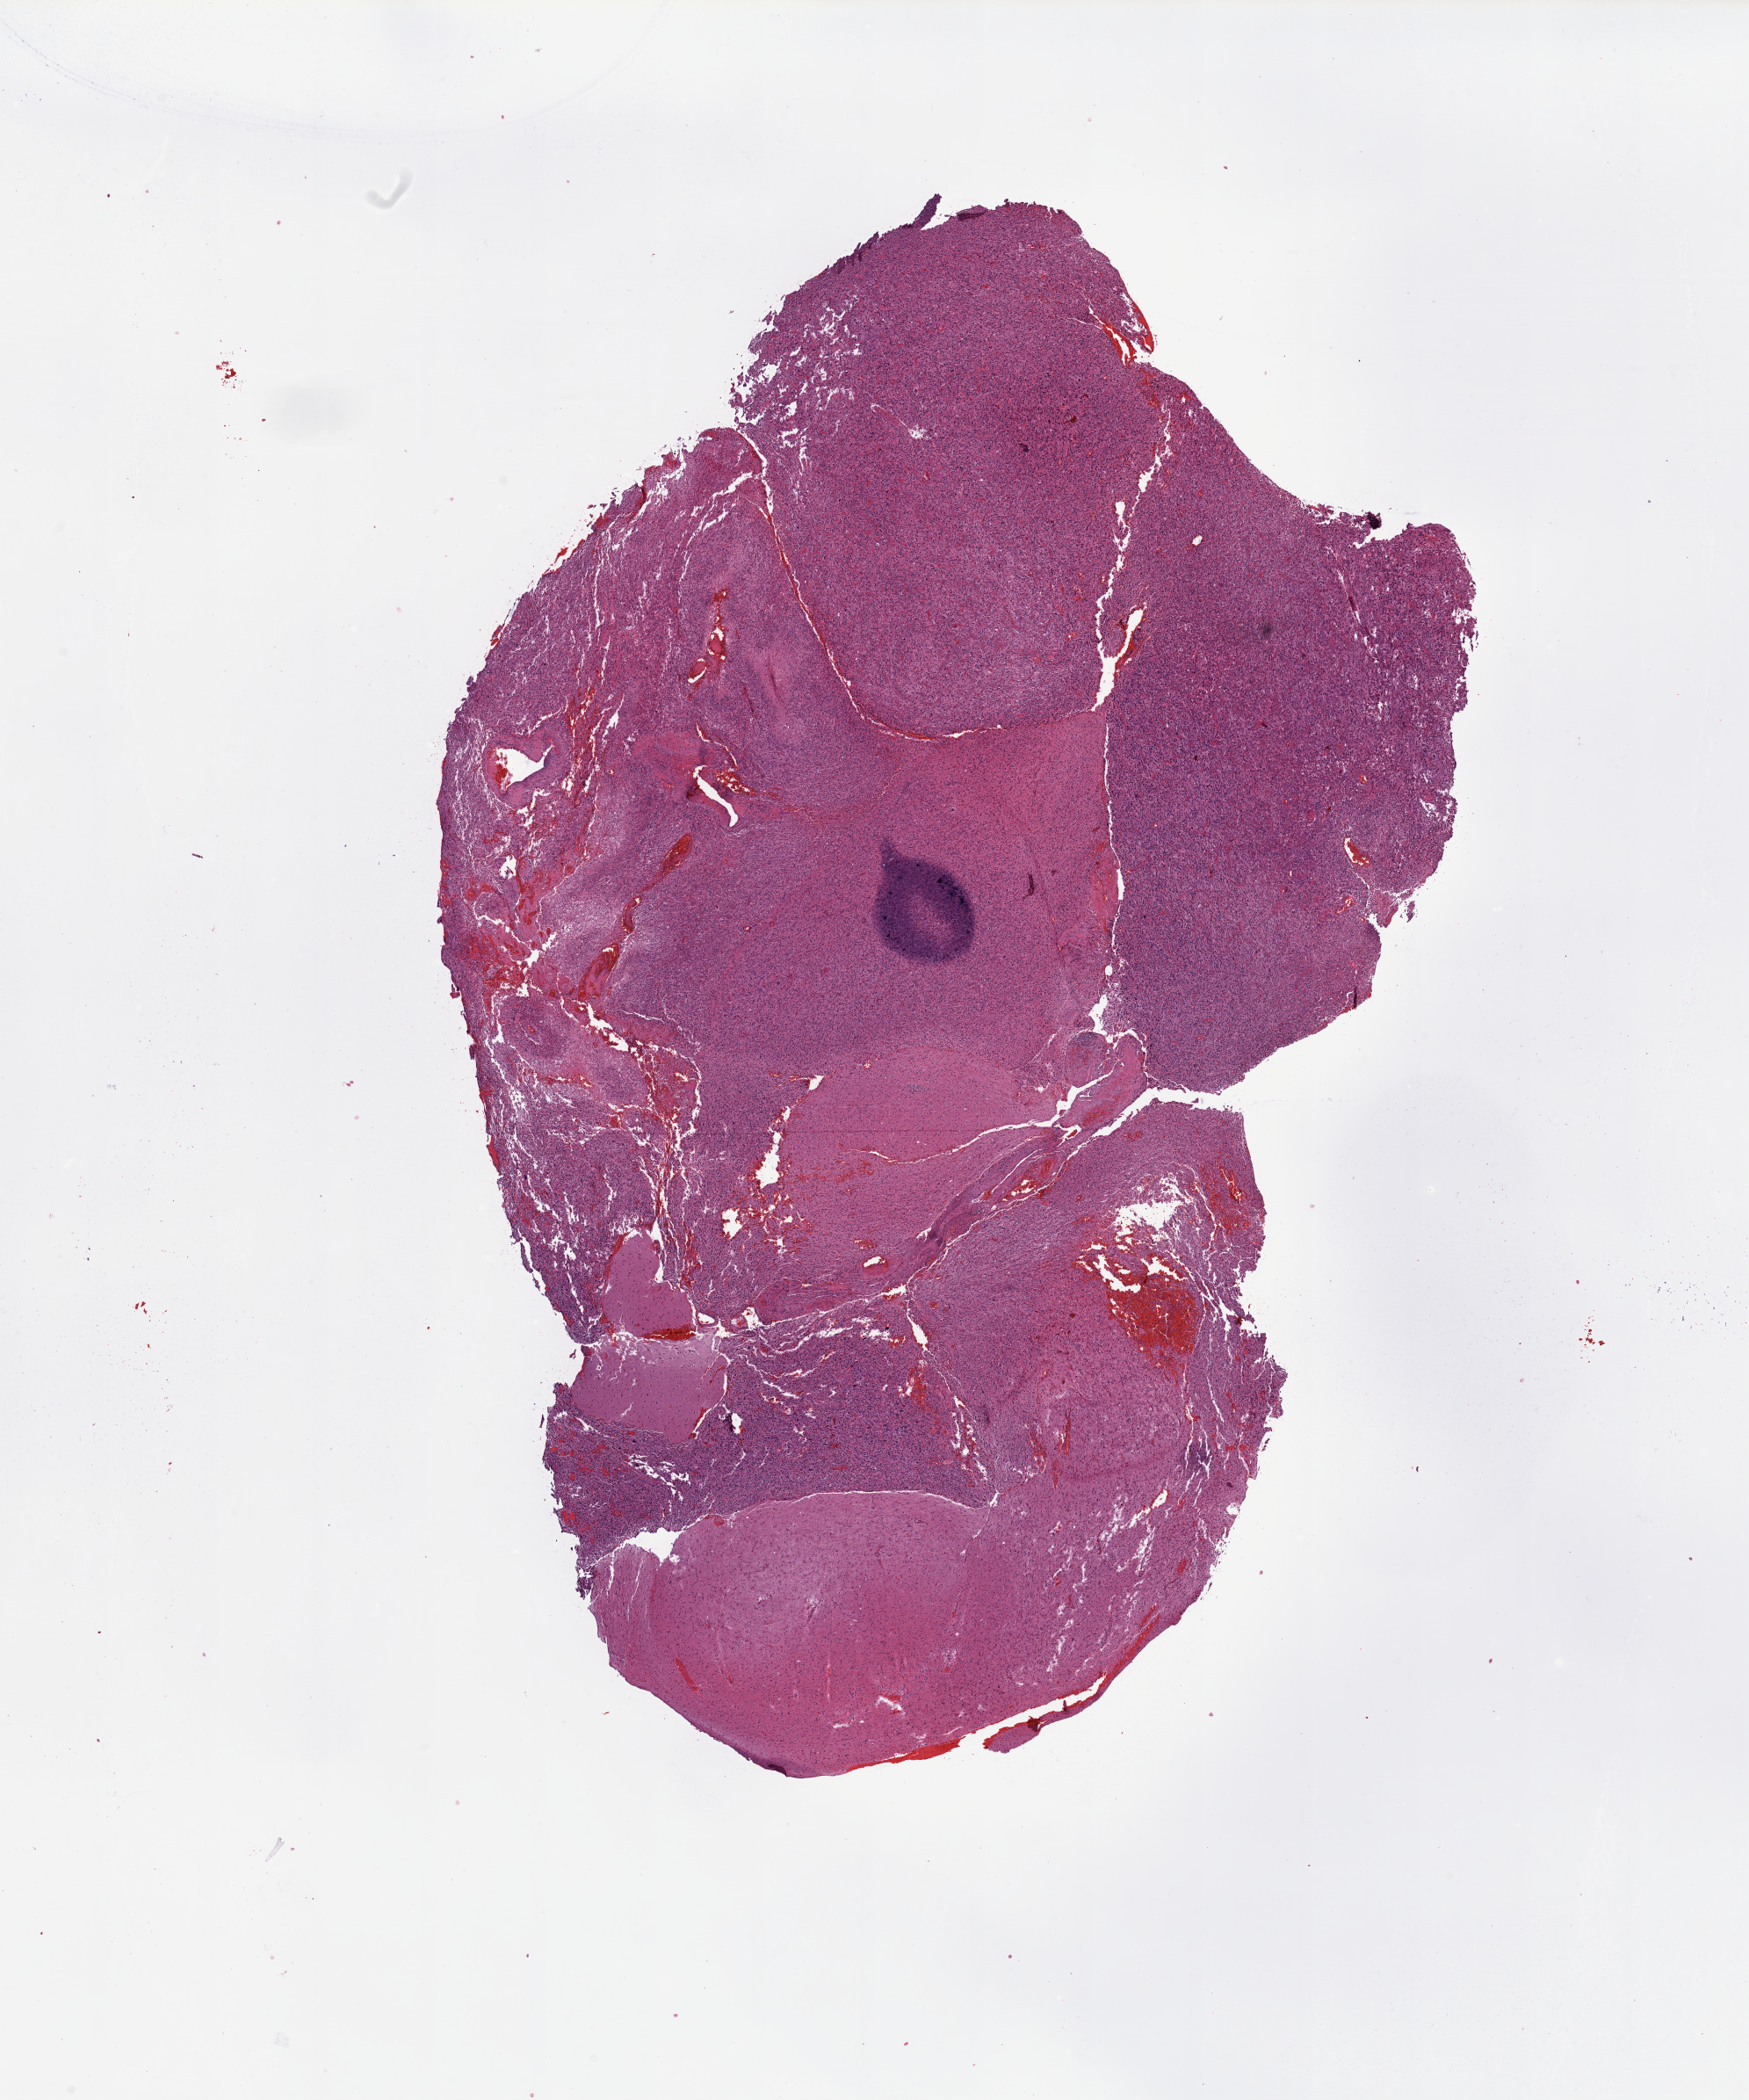
Whole-slide histology image, Hematoxylin and eosin (H&E) stained, a low-resolution overview of the entire scanned area, about 15.8 x 18.9 mm (from a 20x scan). Tumour tissue sample, sampled site: brain. Patient: male, age 58 years. Composition of this section per pathologist review: tumour nuclei 85%, necrosis 5%.
Diagnosis: Glioblastoma. Primary tumour site (as recorded): temporal lobe.